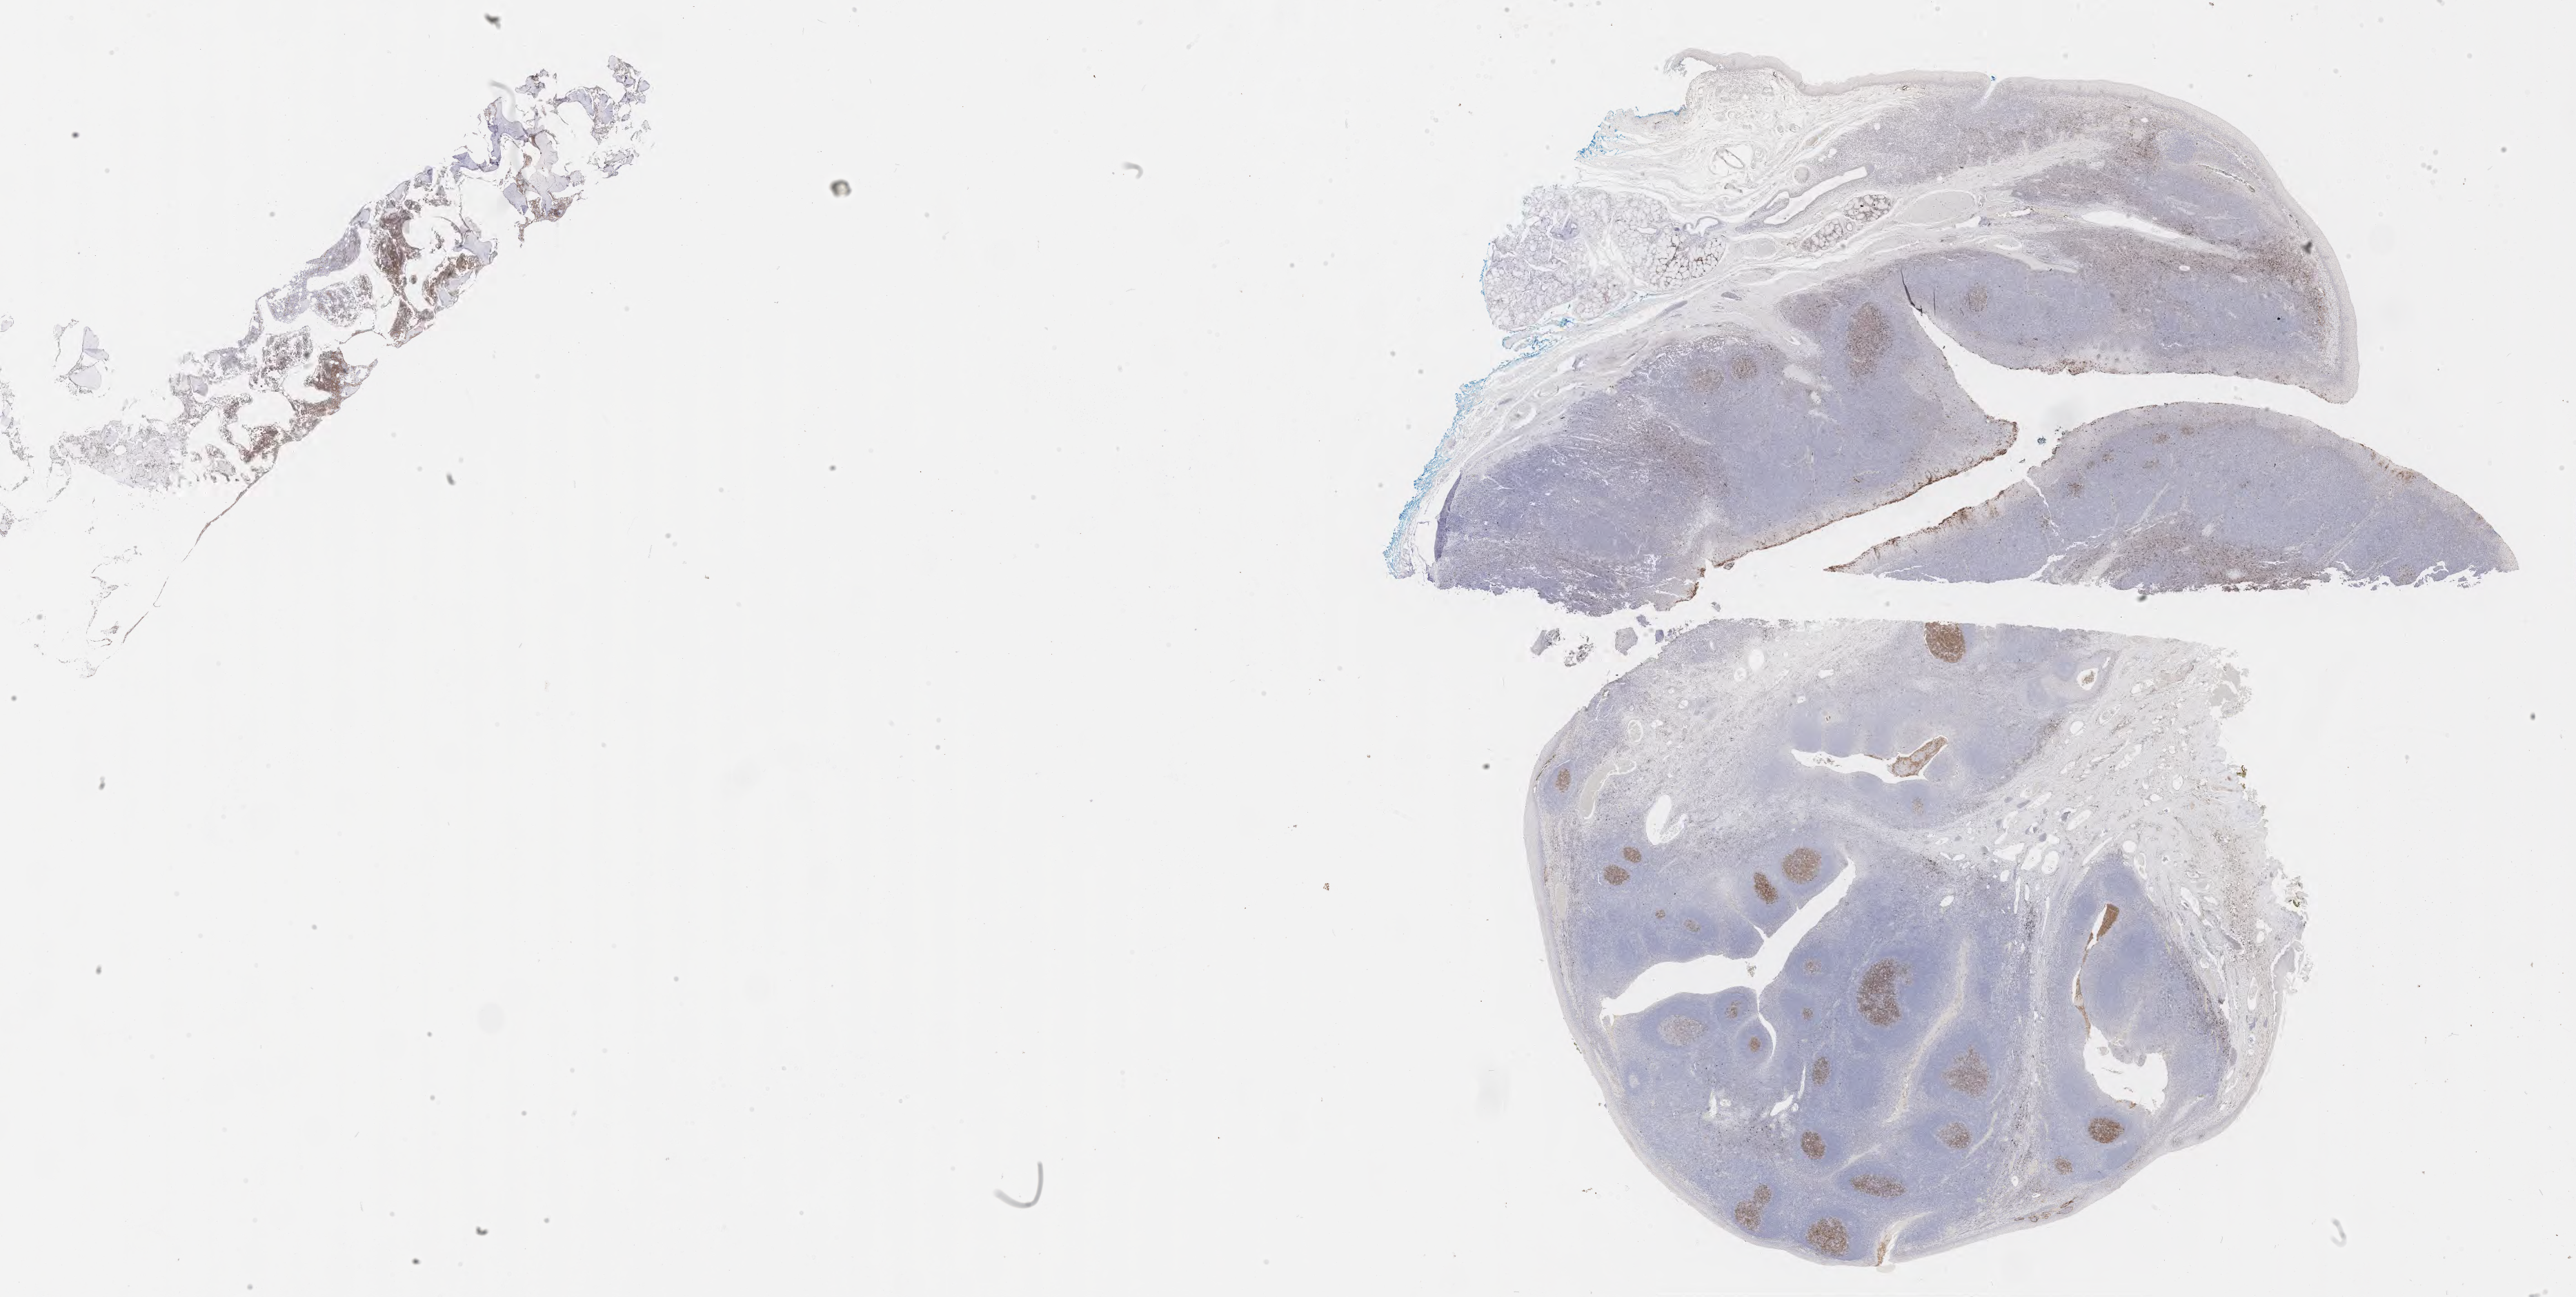
Whole-slide image, immunohistochemical stain for CD10, shown as a low-resolution overview of the whole scanned area (about 30.2 x 15.2 mm). Specimen: tumor tissue. Patient: male, aged 13.
Histologic diagnosis: Burkitt lymphoma, NOS.